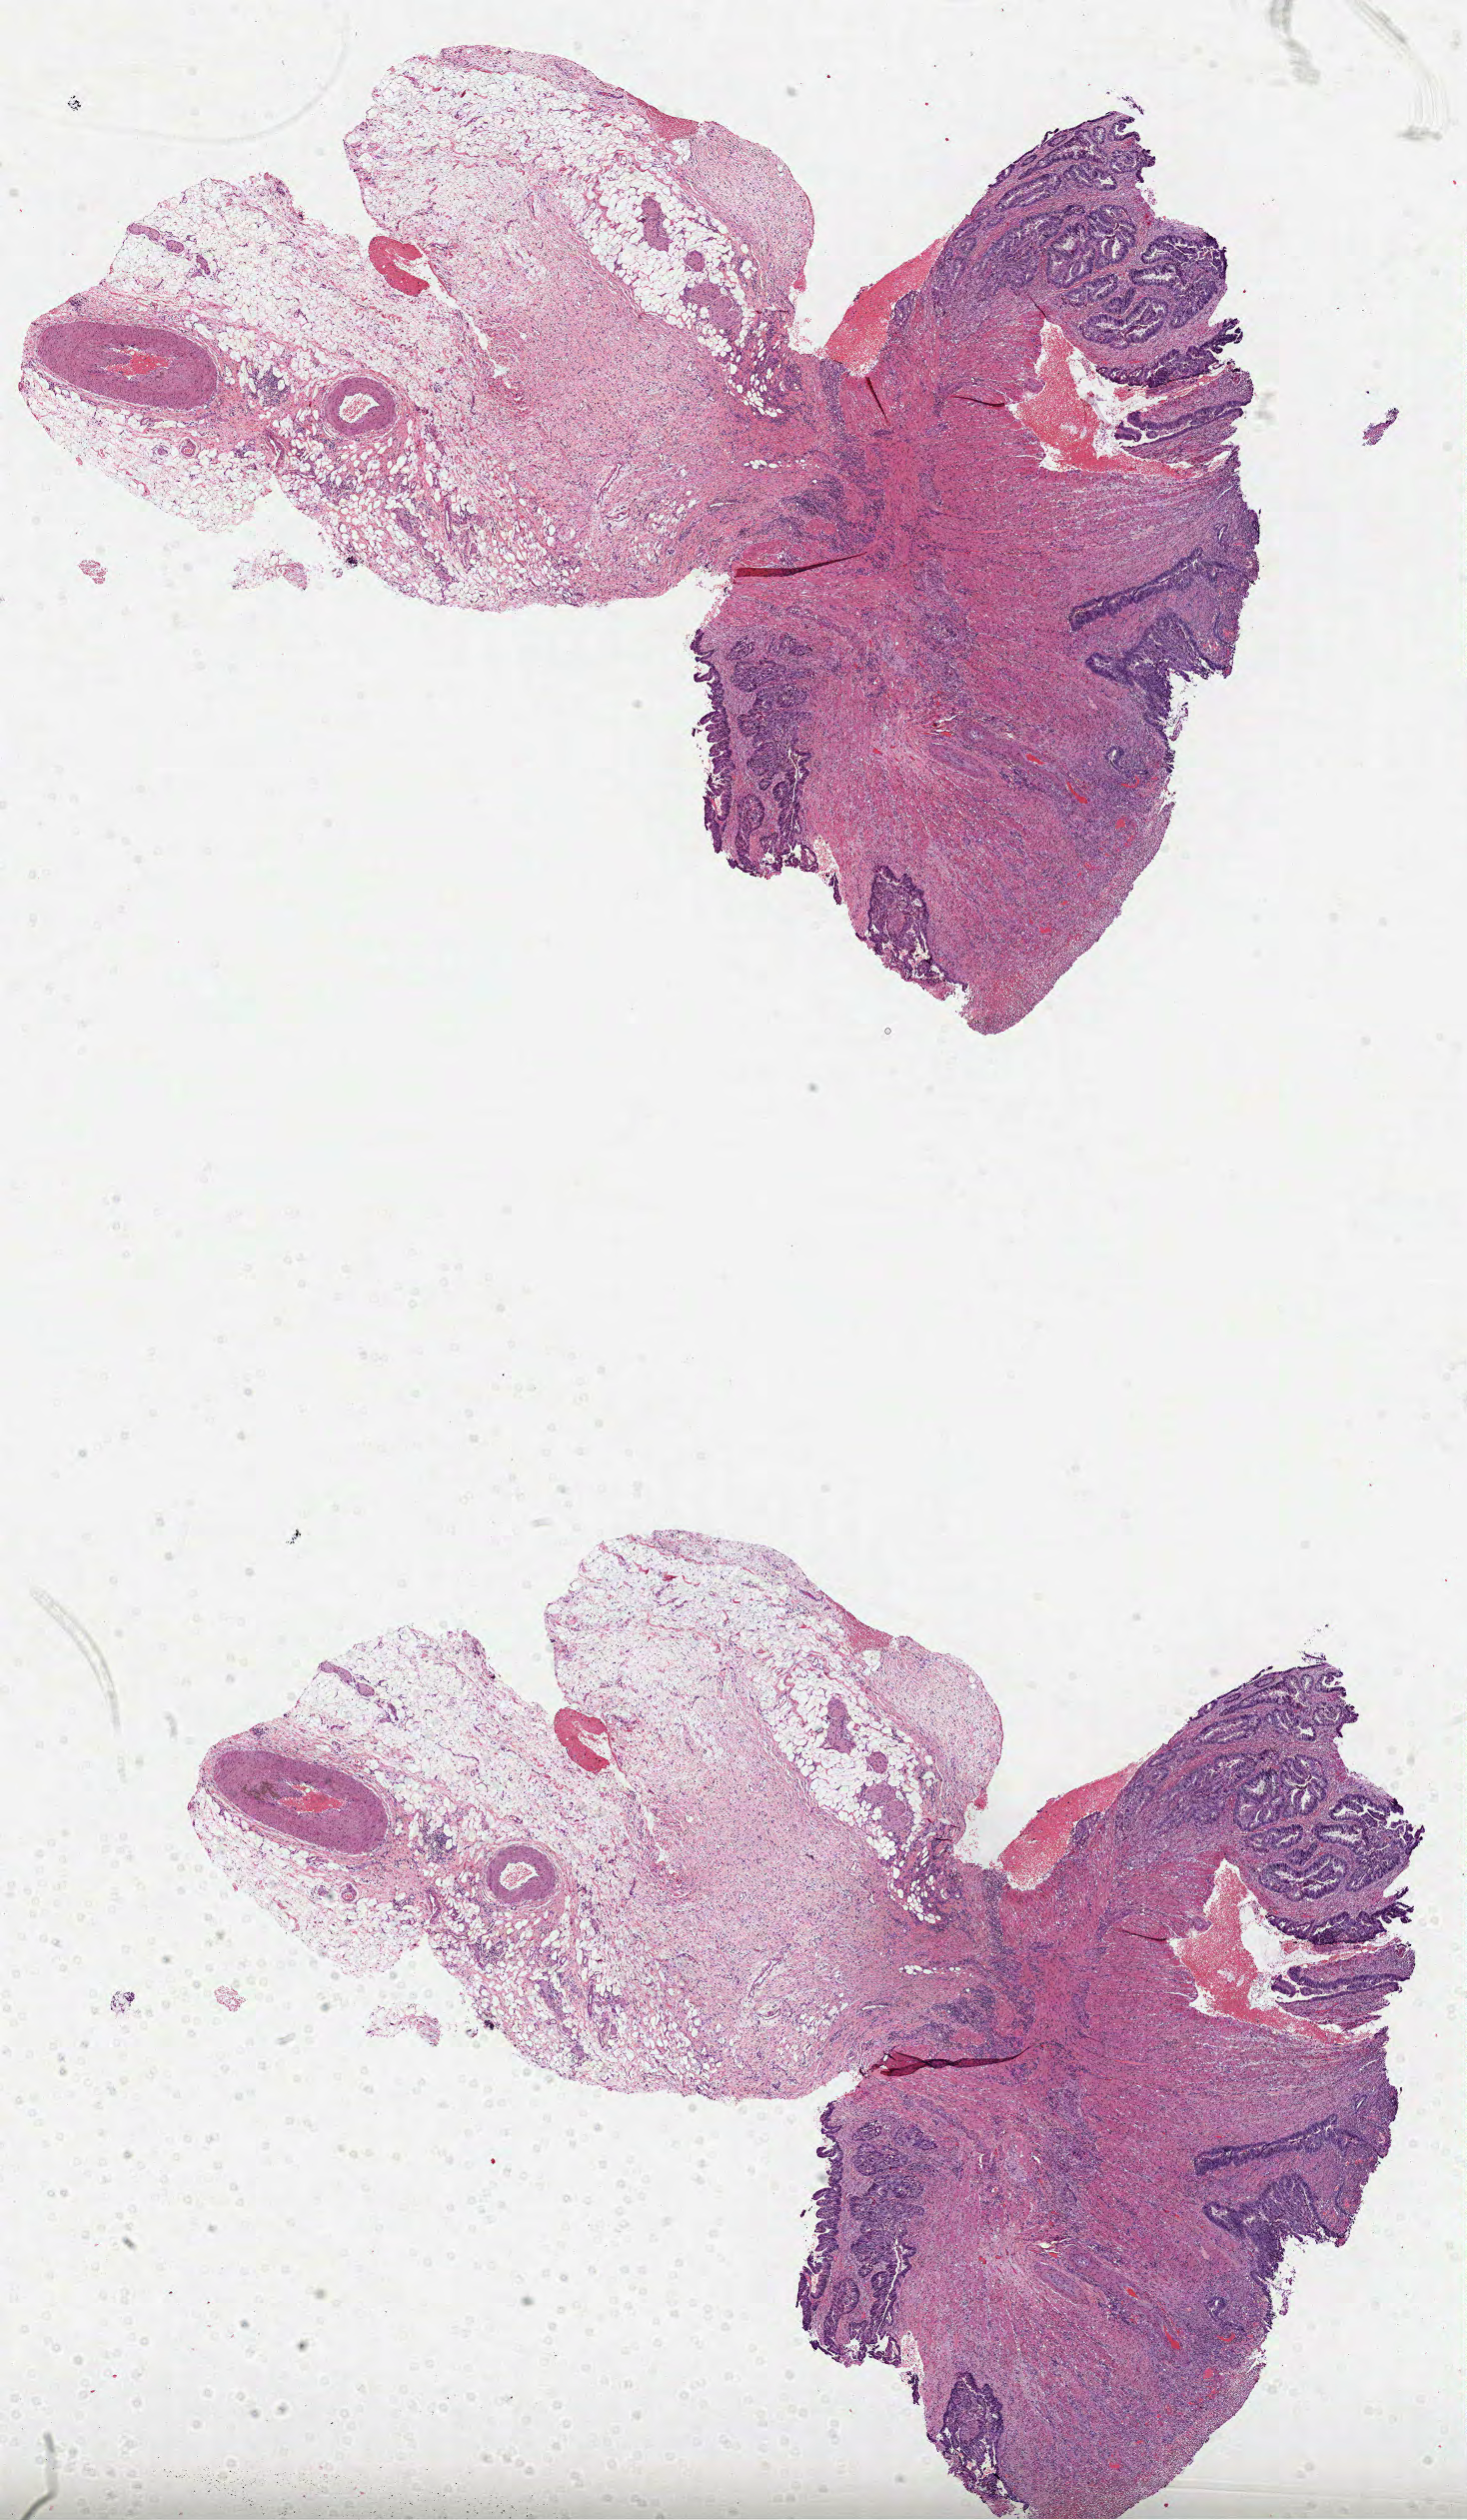
Hematoxylin and eosin (H&E) stained whole-slide image, a low-resolution overview of the entire scanned area, about 11.8 x 20.3 mm. Formalin-fixed paraffin-embedded (FFPE) diagnostic section. Sample: primary tumour, rectum. Patient: male, age at initial diagnosis 57 years.
TNM: T3 N2 M0. Histologic diagnosis: Adenocarcinoma, NOS (rectosigmoid junction). Lymph nodes positive (case pathology): 6 of 16 examined. AJCC pathologic stage: IIIC.